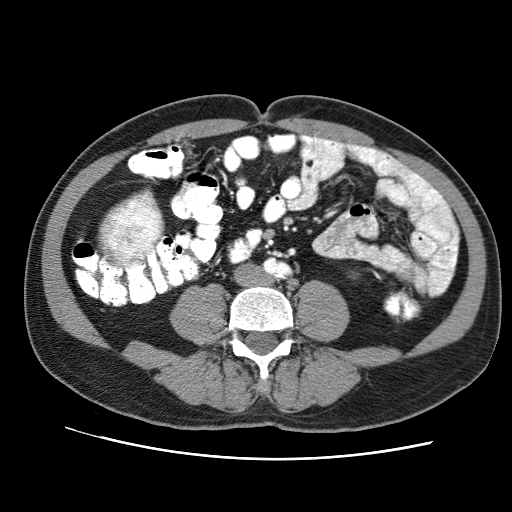
Contrast-enhanced abdominal CT (liver protocol), one axial slice; position 6 of 71 along the scan axis; reconstruction kernel STANDARD; soft-tissue window (W 400 / L 40 HU); 2.5 mm slice thickness; 512 × 512 image matrix. From the clinical record (not read from this slice): diagnosis: hepatocellular carcinoma (patient treated with transarterial chemoembolisation; whether this scan precedes or follows treatment is not stated here); TNM stage (as recorded): Stage-II; Child-Pugh class: A; tumour nodularity: multinodular.
Structures marked on this image (semi-automatic segmentation, software-assisted and operator-edited):
- mass: box from (x=102, y=198) to (x=158, y=263) px